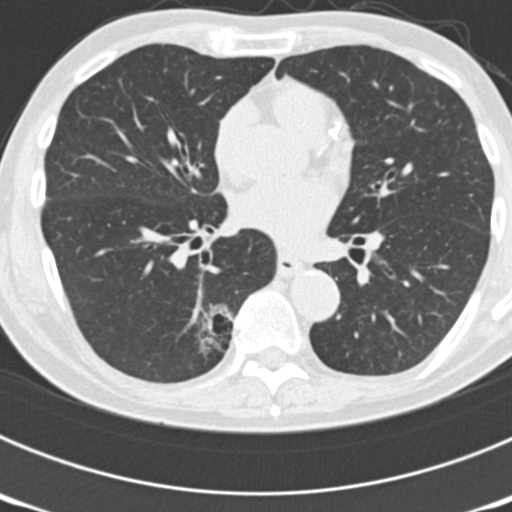
Low-dose screening chest CT, axial slice; third annual screen; lung window (W 1500 / L -600 HU); standard (soft-tissue) reconstruction kernel (B30f); 120 kVp. Male, age 70 years at enrolment. Current smoker at enrolment.
Lesion marked by an expert reader, bounding box [x1, y1, x2, y2] px = [149, 300, 239, 384]. The screening reader recorded 3 non-calcified nodules or masses ≥4 mm on this exam (right upper lobe, left upper lobe, right lower lobe); which of them this box marks is not recorded. Official screen result: positive, other. Later outcome: lung cancer diagnosed 14 days after this screen — bronchiolo-alveolar adenocarcinoma, NOS, right lower lobe, poorly differentiated (G3), stage IB (AJCC 6th edition), 30 mm at pathology.